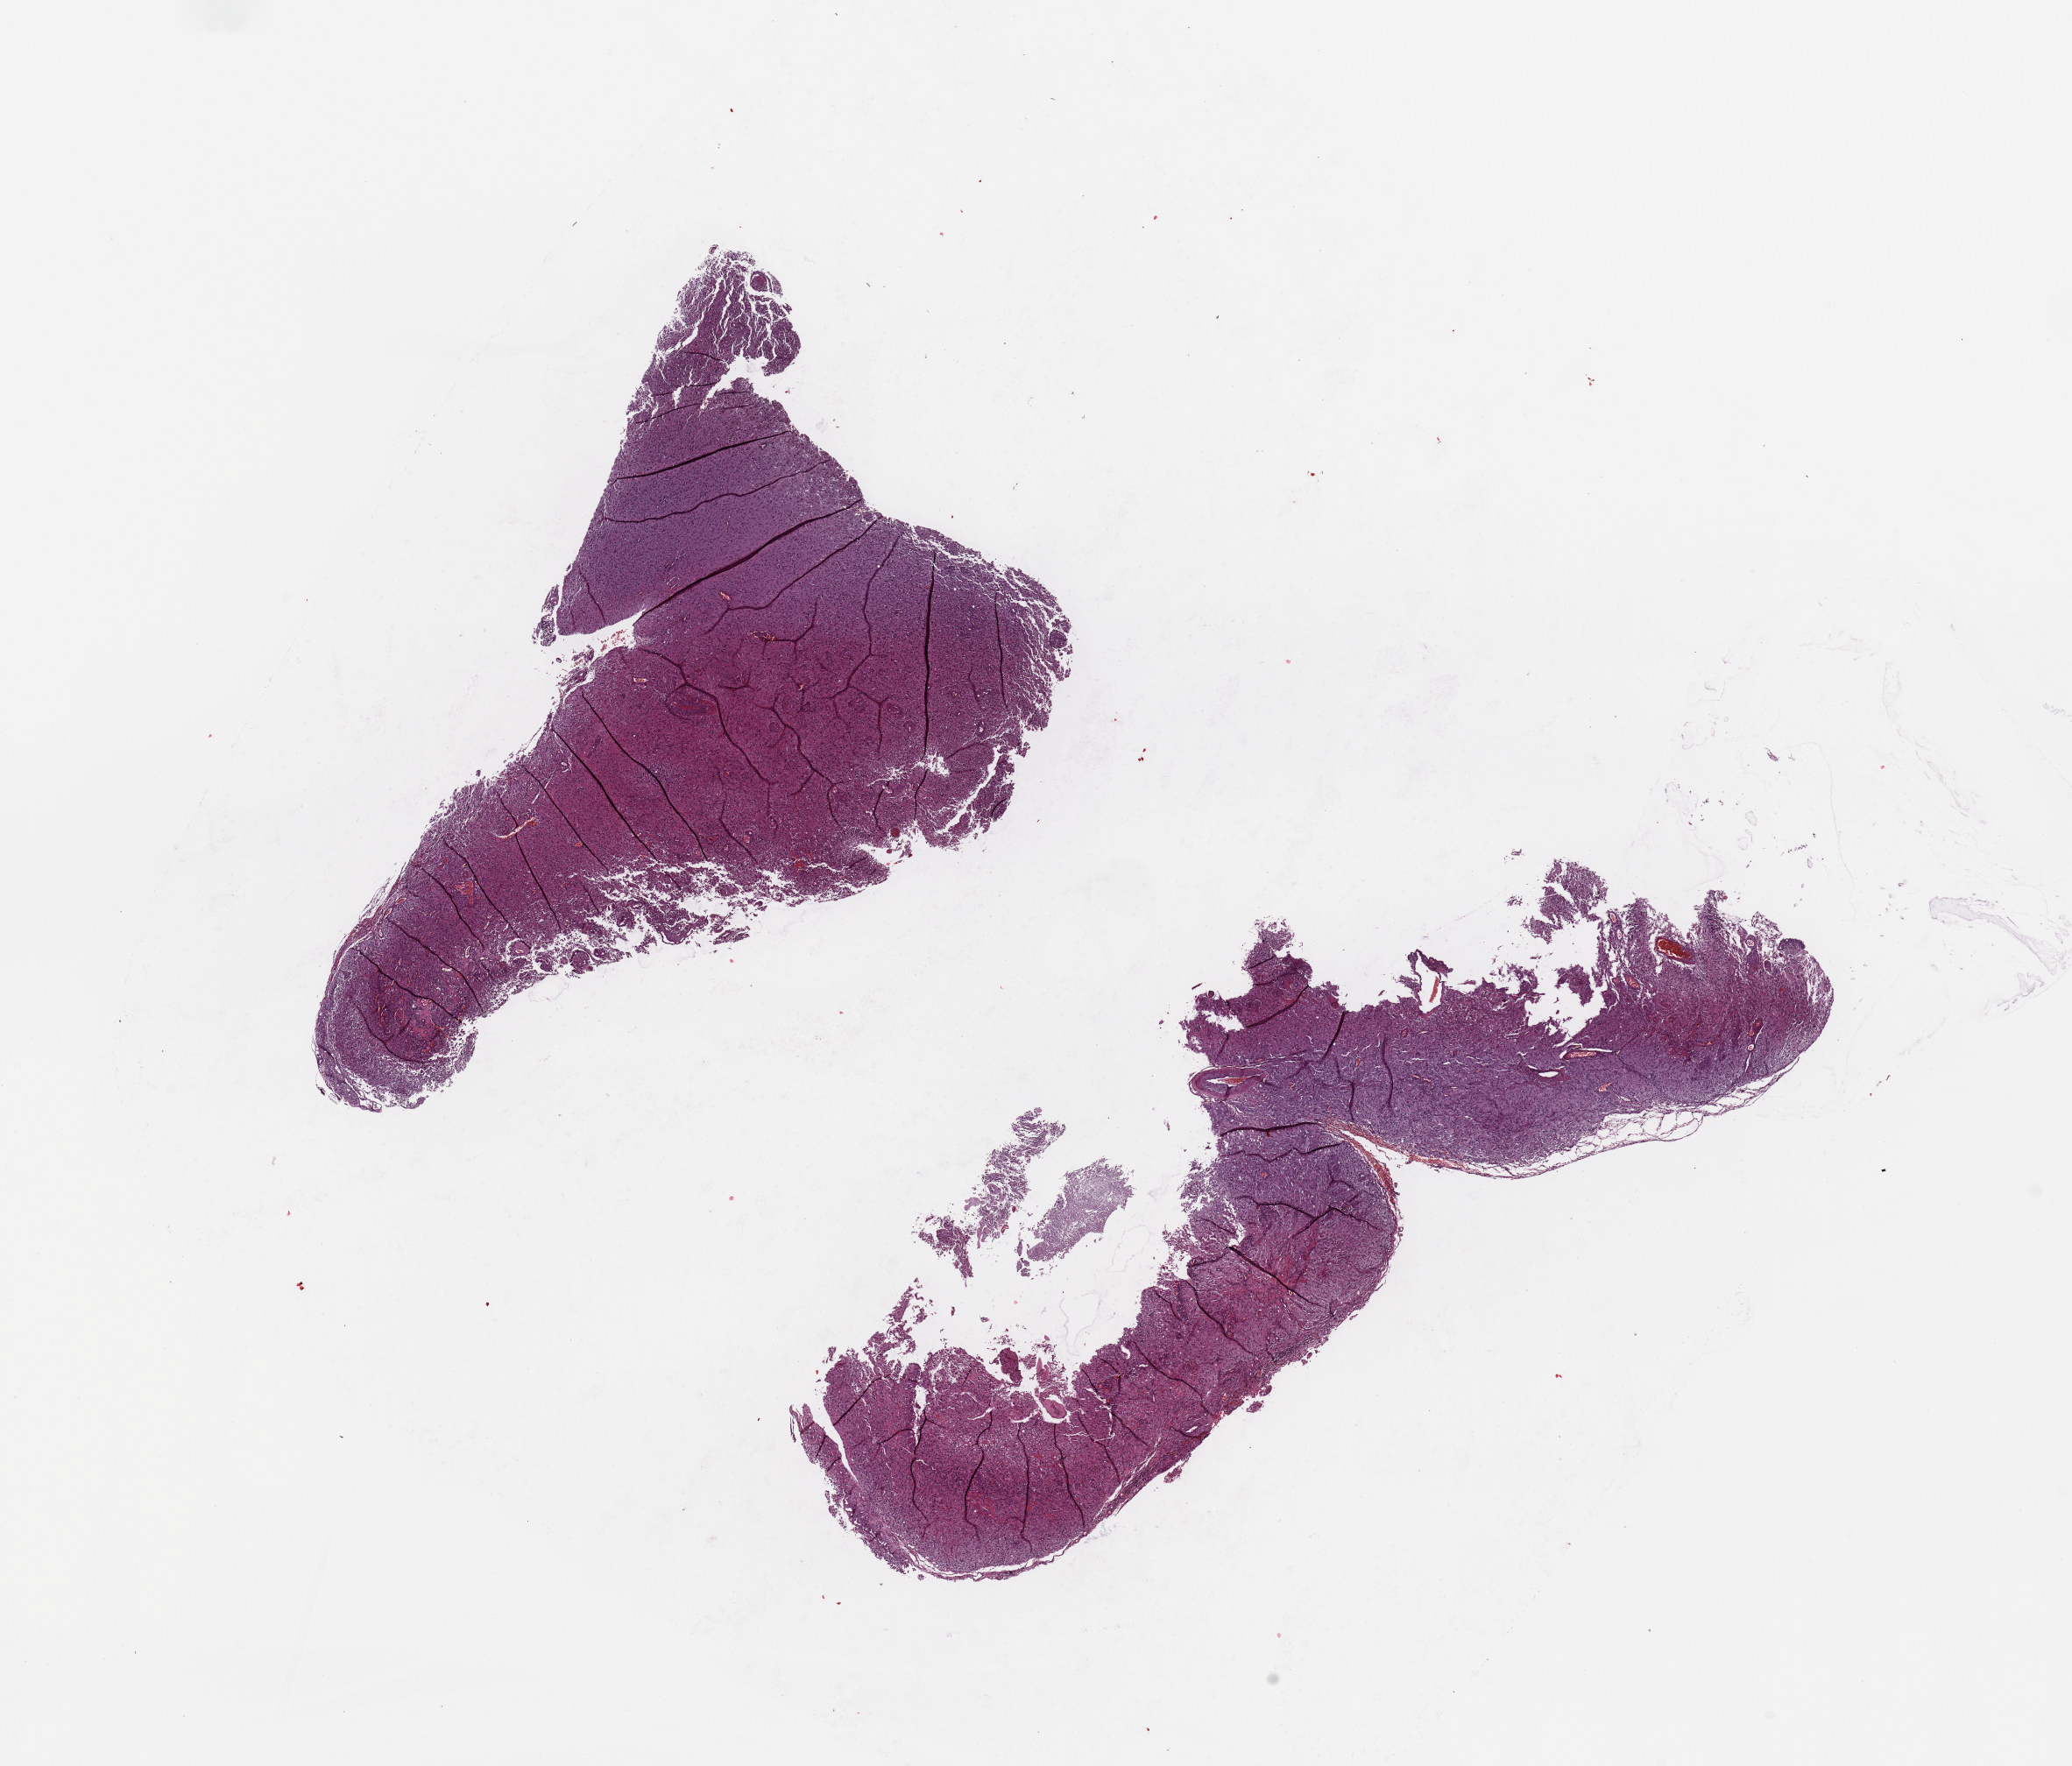
Whole-slide histology image, H&E-stained — a low-resolution overview of the entire scanned area, about 18.7 x 15.9 mm (acquisition: 20x scan); tumour tissue sample, sampled site: brain. Patient: male, age 59 years. Composition of this section per pathologist review: tumour nuclei 80%, necrosis 2%.
* diagnosis: Glioblastoma
* primary tumour site (as recorded): temporal lobe